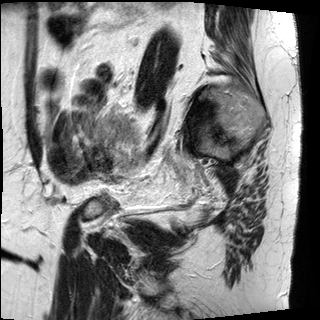
Pelvic MRI for cervical cancer, one sagittal slice; slice 25 of 30 in the series (ordered by position); T2-weighted; 1.5 T; TE 89 ms, TR 2930 ms; 4 mm slice thickness; 320 × 320 image matrix, field of view 260 × 260 mm. Patient: female, 62 years.
Outlined on this slice (outlined manually by an expert reader):
- uterus and cervix: bounding box (x1, y1, x2, y2) in pixels: (109, 116, 132, 138)